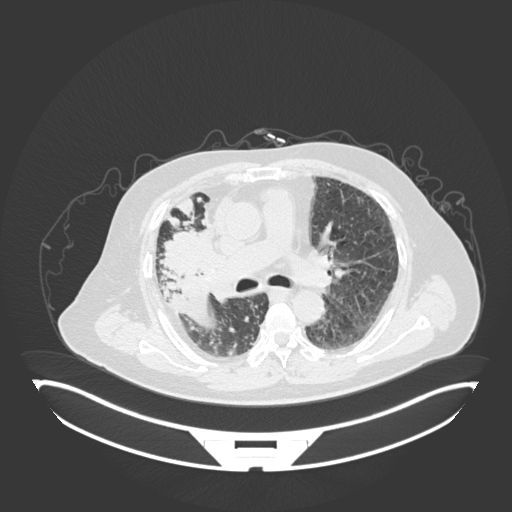
Chest CT, one axial slice; position 101 of 201 along the scan axis; reconstruction kernel B30f; 120 kVp; lung window (W 1500 / L -600 HU); 512 × 512 image matrix. Patient: male, 69 years. Case-level facts recorded for this patient, not image findings: clinical TNM (as recorded): T4 N3 M1.
Annotated regions visible in this slice (rectangle marked by the reading radiologist):
- lung tumour (recorded histology: adenocarcinoma): bounding box <155,225,212,281> (left, top, right, bottom; pixels)